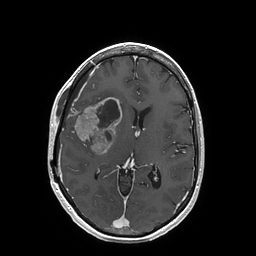
Brain MRI from a brain-tumour surgery series, one axial slice; position 83 of 202 along the scan axis; T1-weighted post-contrast; 1 mm slice thickness; 256 × 256 image matrix, field of view 250 × 250 mm. From the clinical record (not read from this slice): histopathology: Glioblastoma; WHO grade: 4; IDH mutation: no.
Structures marked on this image (manually delineated by an expert):
- tumour: bounding box (x1, y1, x2, y2) in pixels: (70, 98, 122, 155)